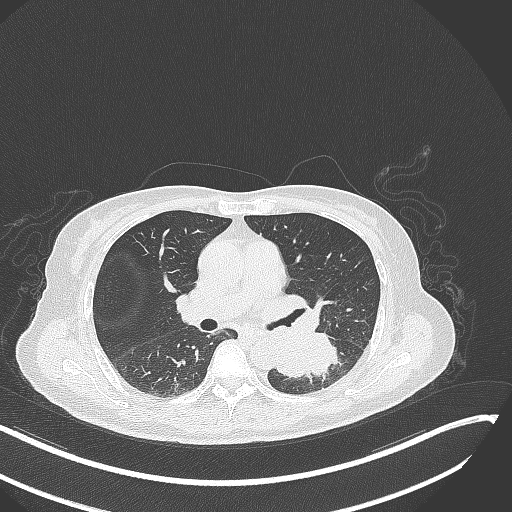
Chest CT, one axial slice. Slice 157 of 342 in the series (ordered by position). Lung window (W 1500 / L -600 HU). 512 × 512 image matrix. Female patient, age 64 years. Case-level facts recorded for this patient, not image findings: clinical TNM (as recorded): T3 N1 M1; histopathological grade: G3.
Structures marked on this image (bounding box drawn by a radiologist):
- lung tumour (recorded histology: small cell carcinoma): bounding box <272,324,343,388> (left, top, right, bottom; pixels)